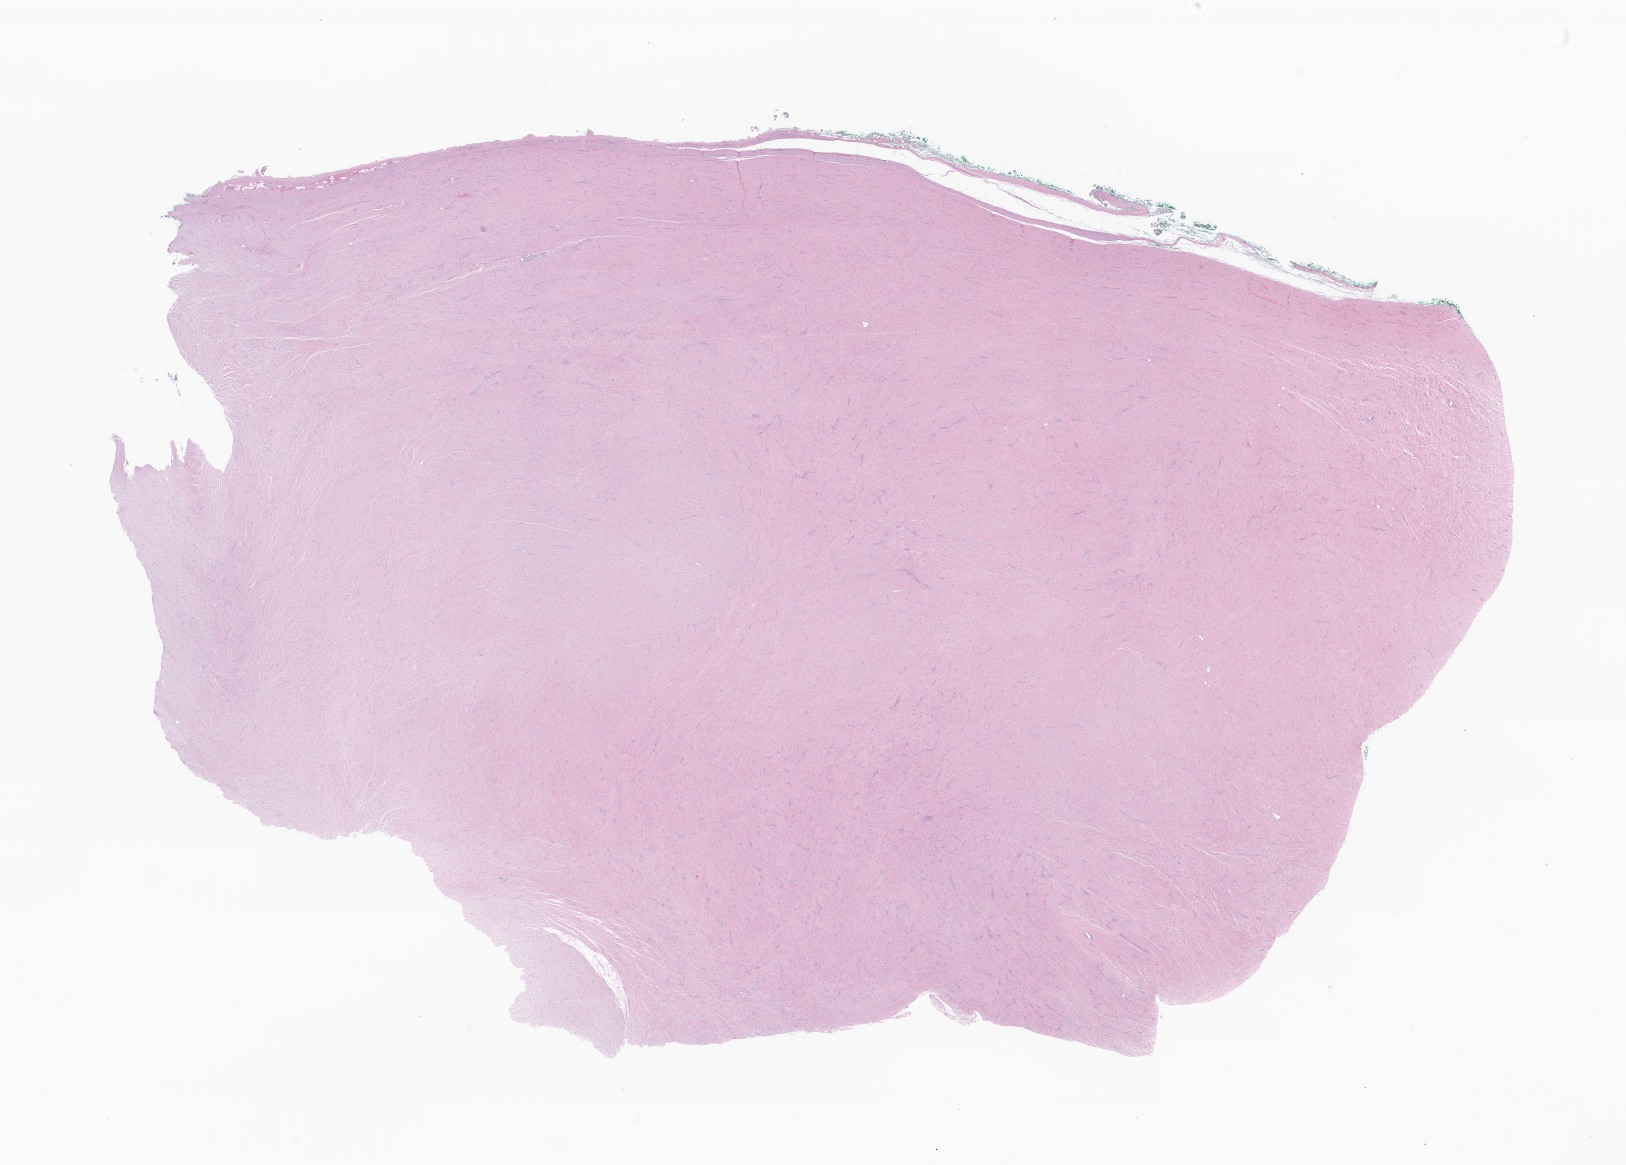
Digitized hematoxylin and eosin (H&E)-stained section of tumor tissue from the abdomen — shown as a low-resolution overview of the whole scanned area (about 27.4 x 19.7 mm). FFPE section. Patient: female, age 104 months (8 years 8 months).
* diagnosis: Neoplasm, uncertain whether benign or malignant